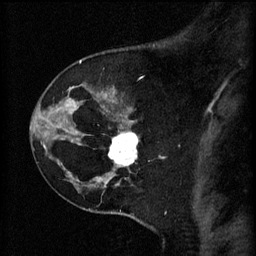
Breast MRI (dynamic contrast-enhanced), one sagittal slice; position 45 of 60 along the scan axis; 3 images stored at this slice position (order not interpretable as contrast timing); 1.5 T; TE 4.2 ms, TR 11 ms; 256 × 256 image matrix, field of view 180 × 180 mm. Patient: female, 45 years.
Annotated regions visible in this slice (semi-automatically segmented with operator editing):
- analysis volume of interest (the breast-tissue region the enhancement analysis was run in; not a lesion): bounding box <110,128,141,171> (left, top, right, bottom; pixels)
- tumour enhancement mask (voxels above the 70 % enhancement threshold inside the analysis volume of interest): <110,132,139,167>